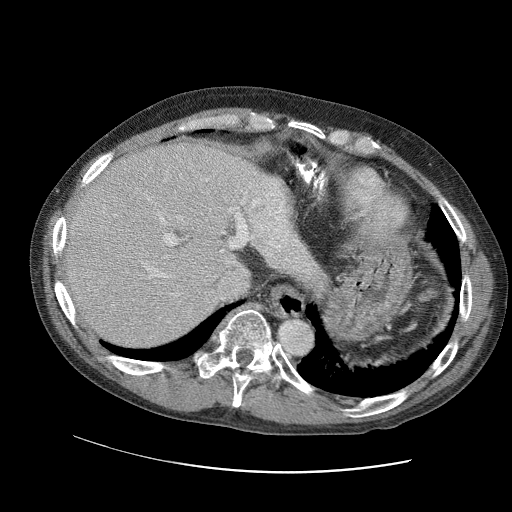
Contrast-enhanced abdominal CT (liver protocol), one axial slice. Slice 79 of 109 in the series (ordered by position). Reconstruction kernel STANDARD. 120 kVp. Soft-tissue window (W 400 / L 40 HU). 512 × 512 image matrix, field of view 400 × 400 mm. Case-level facts recorded for this patient, not image findings: diagnosis: hepatocellular carcinoma (patient treated with transarterial chemoembolisation; whether this scan precedes or follows treatment is not stated here); TNM stage (as recorded): Stage-IIIC; Child-Pugh class: B.
Annotated regions visible in this slice (semi-automatically segmented with operator editing):
- abdominal aorta: bounding box <280,319,311,352> (left, top, right, bottom; pixels)
- liver parenchyma outside the tumour (the mass and vessels are separate outlines, so this box may not span the whole liver): <60,138,314,346>
- liver vessels: <60,161,304,323>